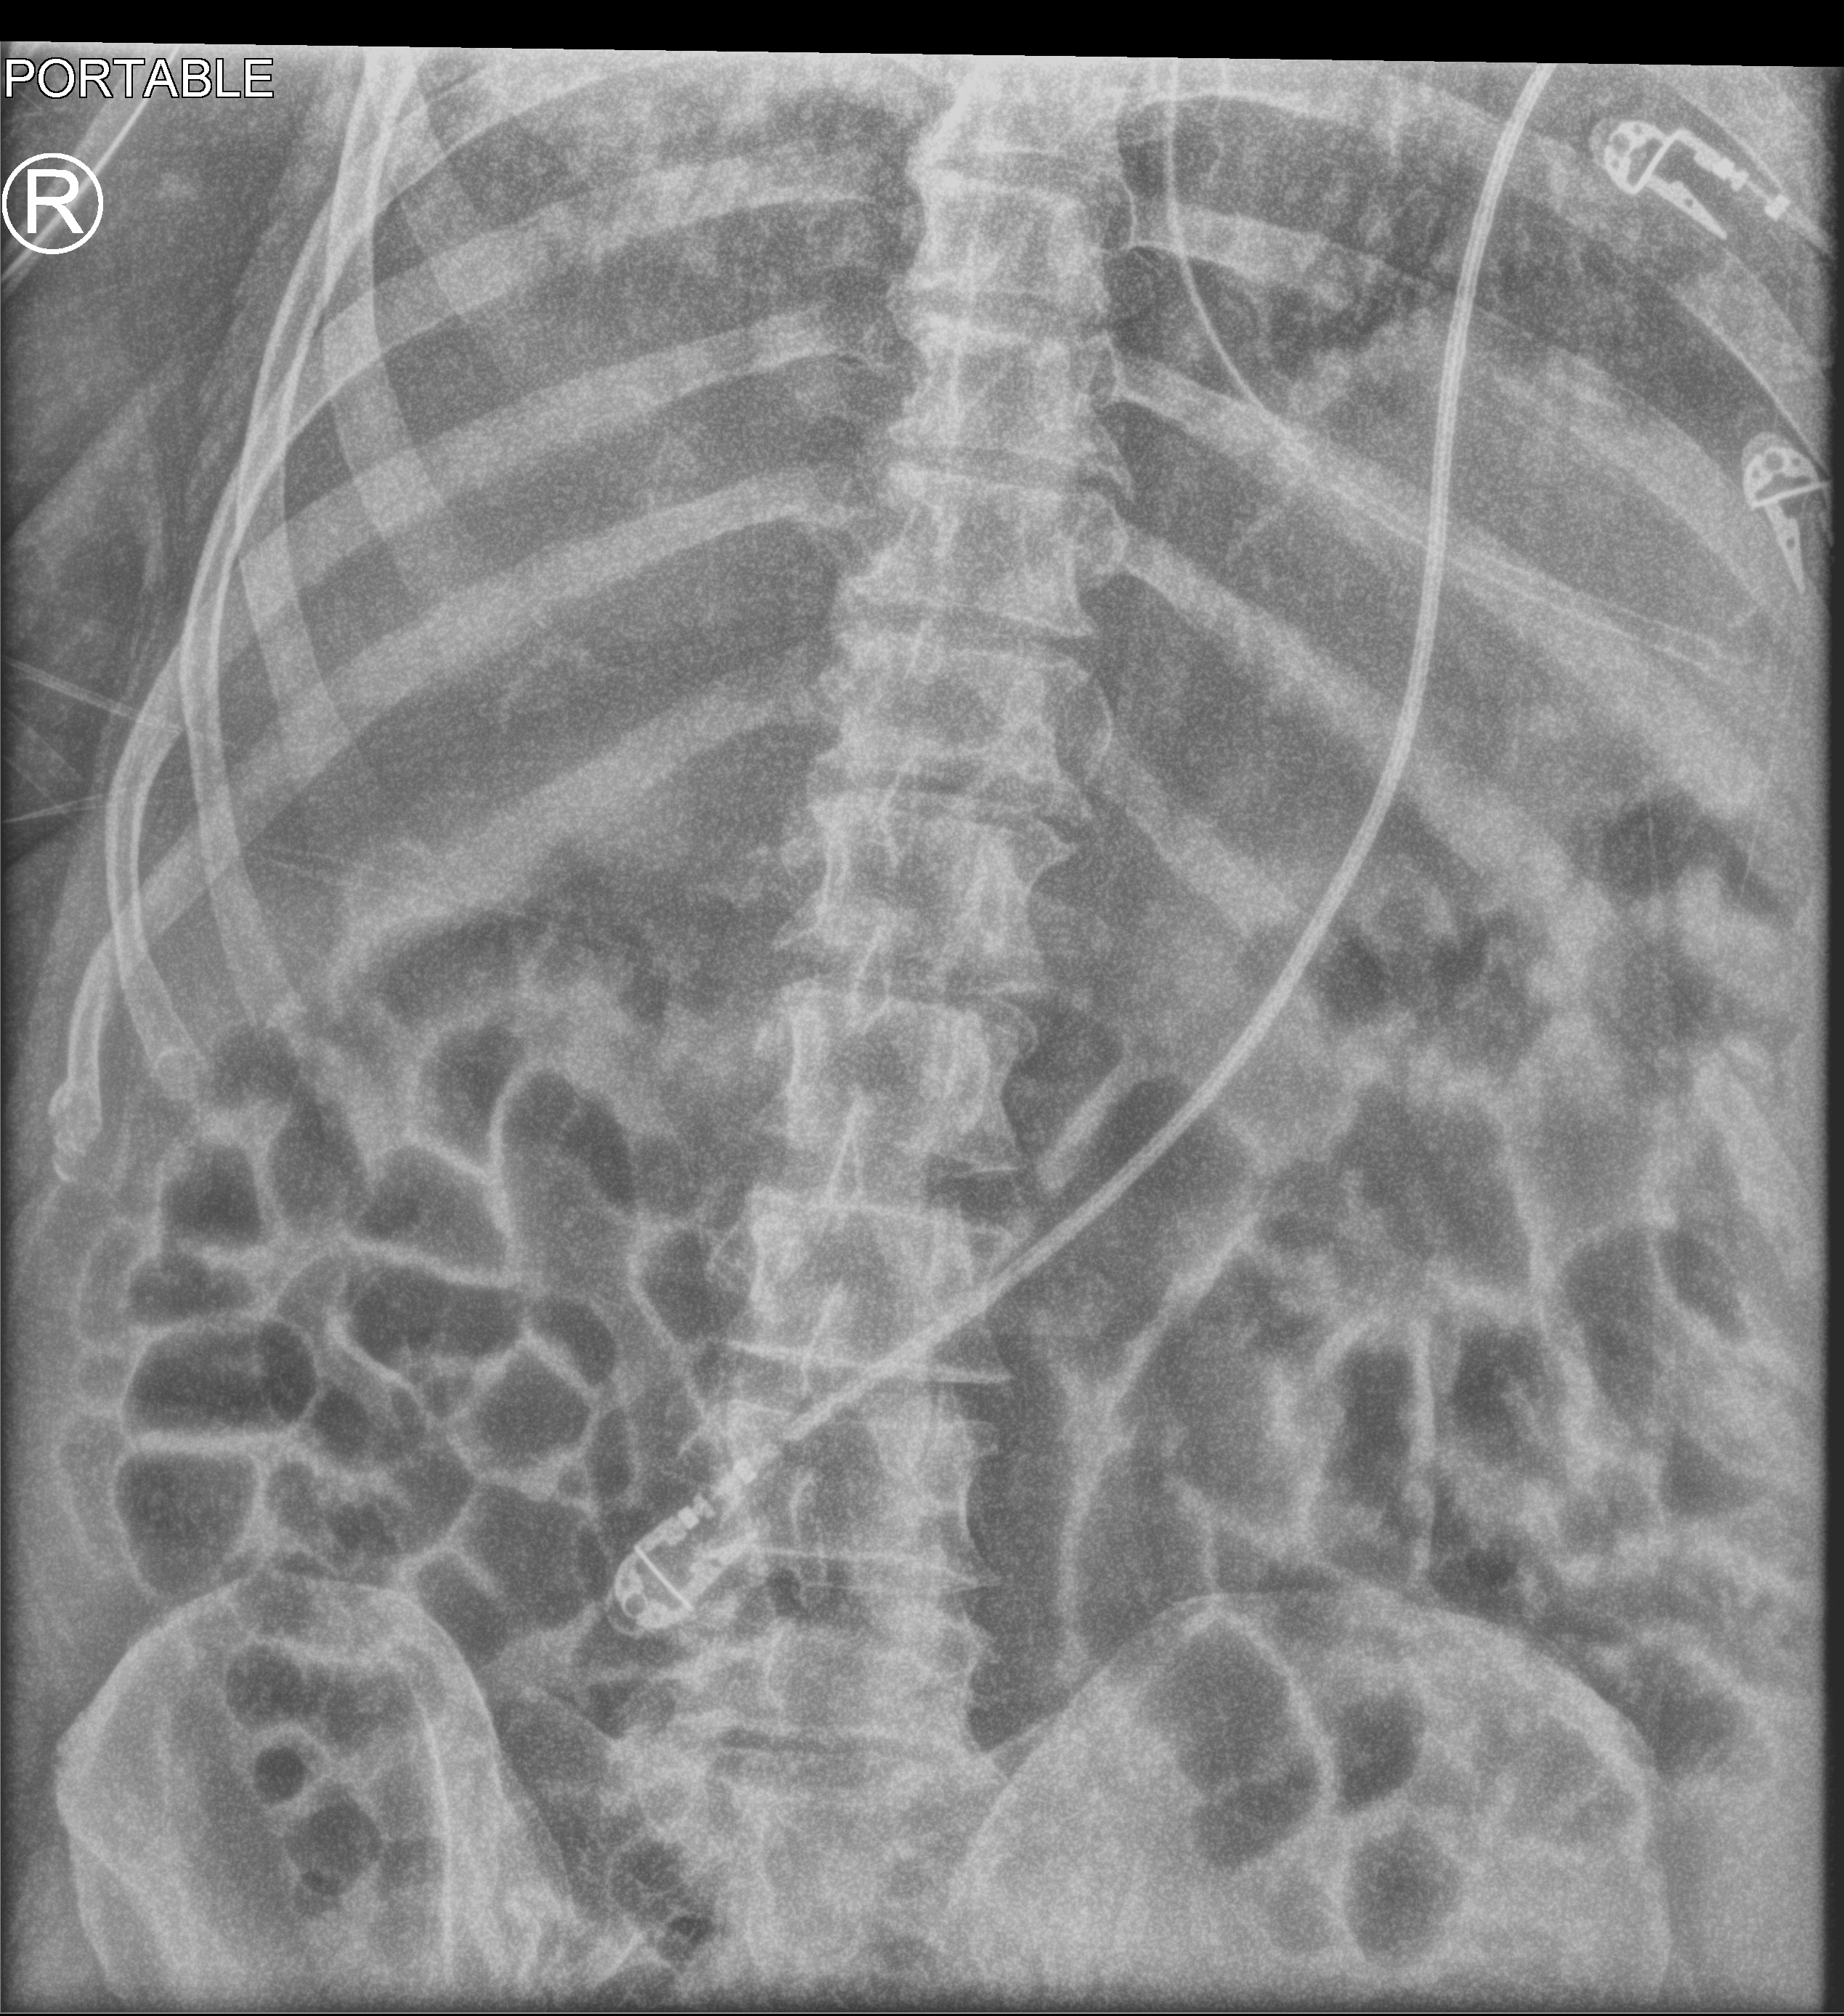
Abdomen X-ray (portable), anteroposterior (AP) projection. Male patient hospitalised with COVID-19, age 60–74 years.
Admission-level facts for this patient (not findings on this image; timing relative to this image not recorded): length of hospital stay: 40 days; admitted to intensive care during this hospital stay: yes; mechanically ventilated during this hospital stay: yes.